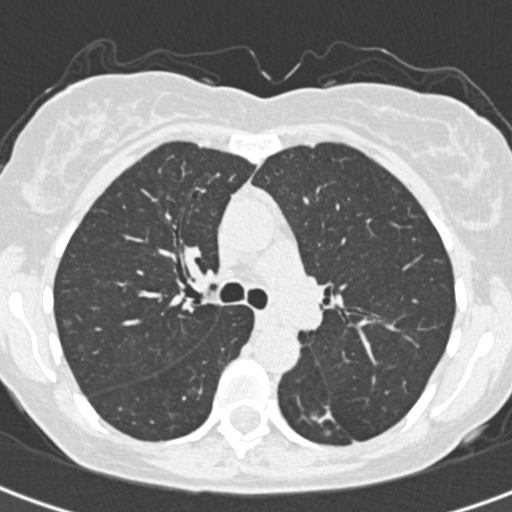
Low-dose screening chest CT, one axial slice; position 215 of 328 along the scan axis; 120 kVp; lung window (W 1500 / L -600 HU); 1 mm slice thickness; 512 × 512 image matrix, field of view 284 × 284 mm.
Structures marked on this image (outlined manually by an expert reader):
- lesion 1 (tumor, lower lobe of left lung): bounding box (x1, y1, x2, y2) in pixels: (315, 409, 331, 422)